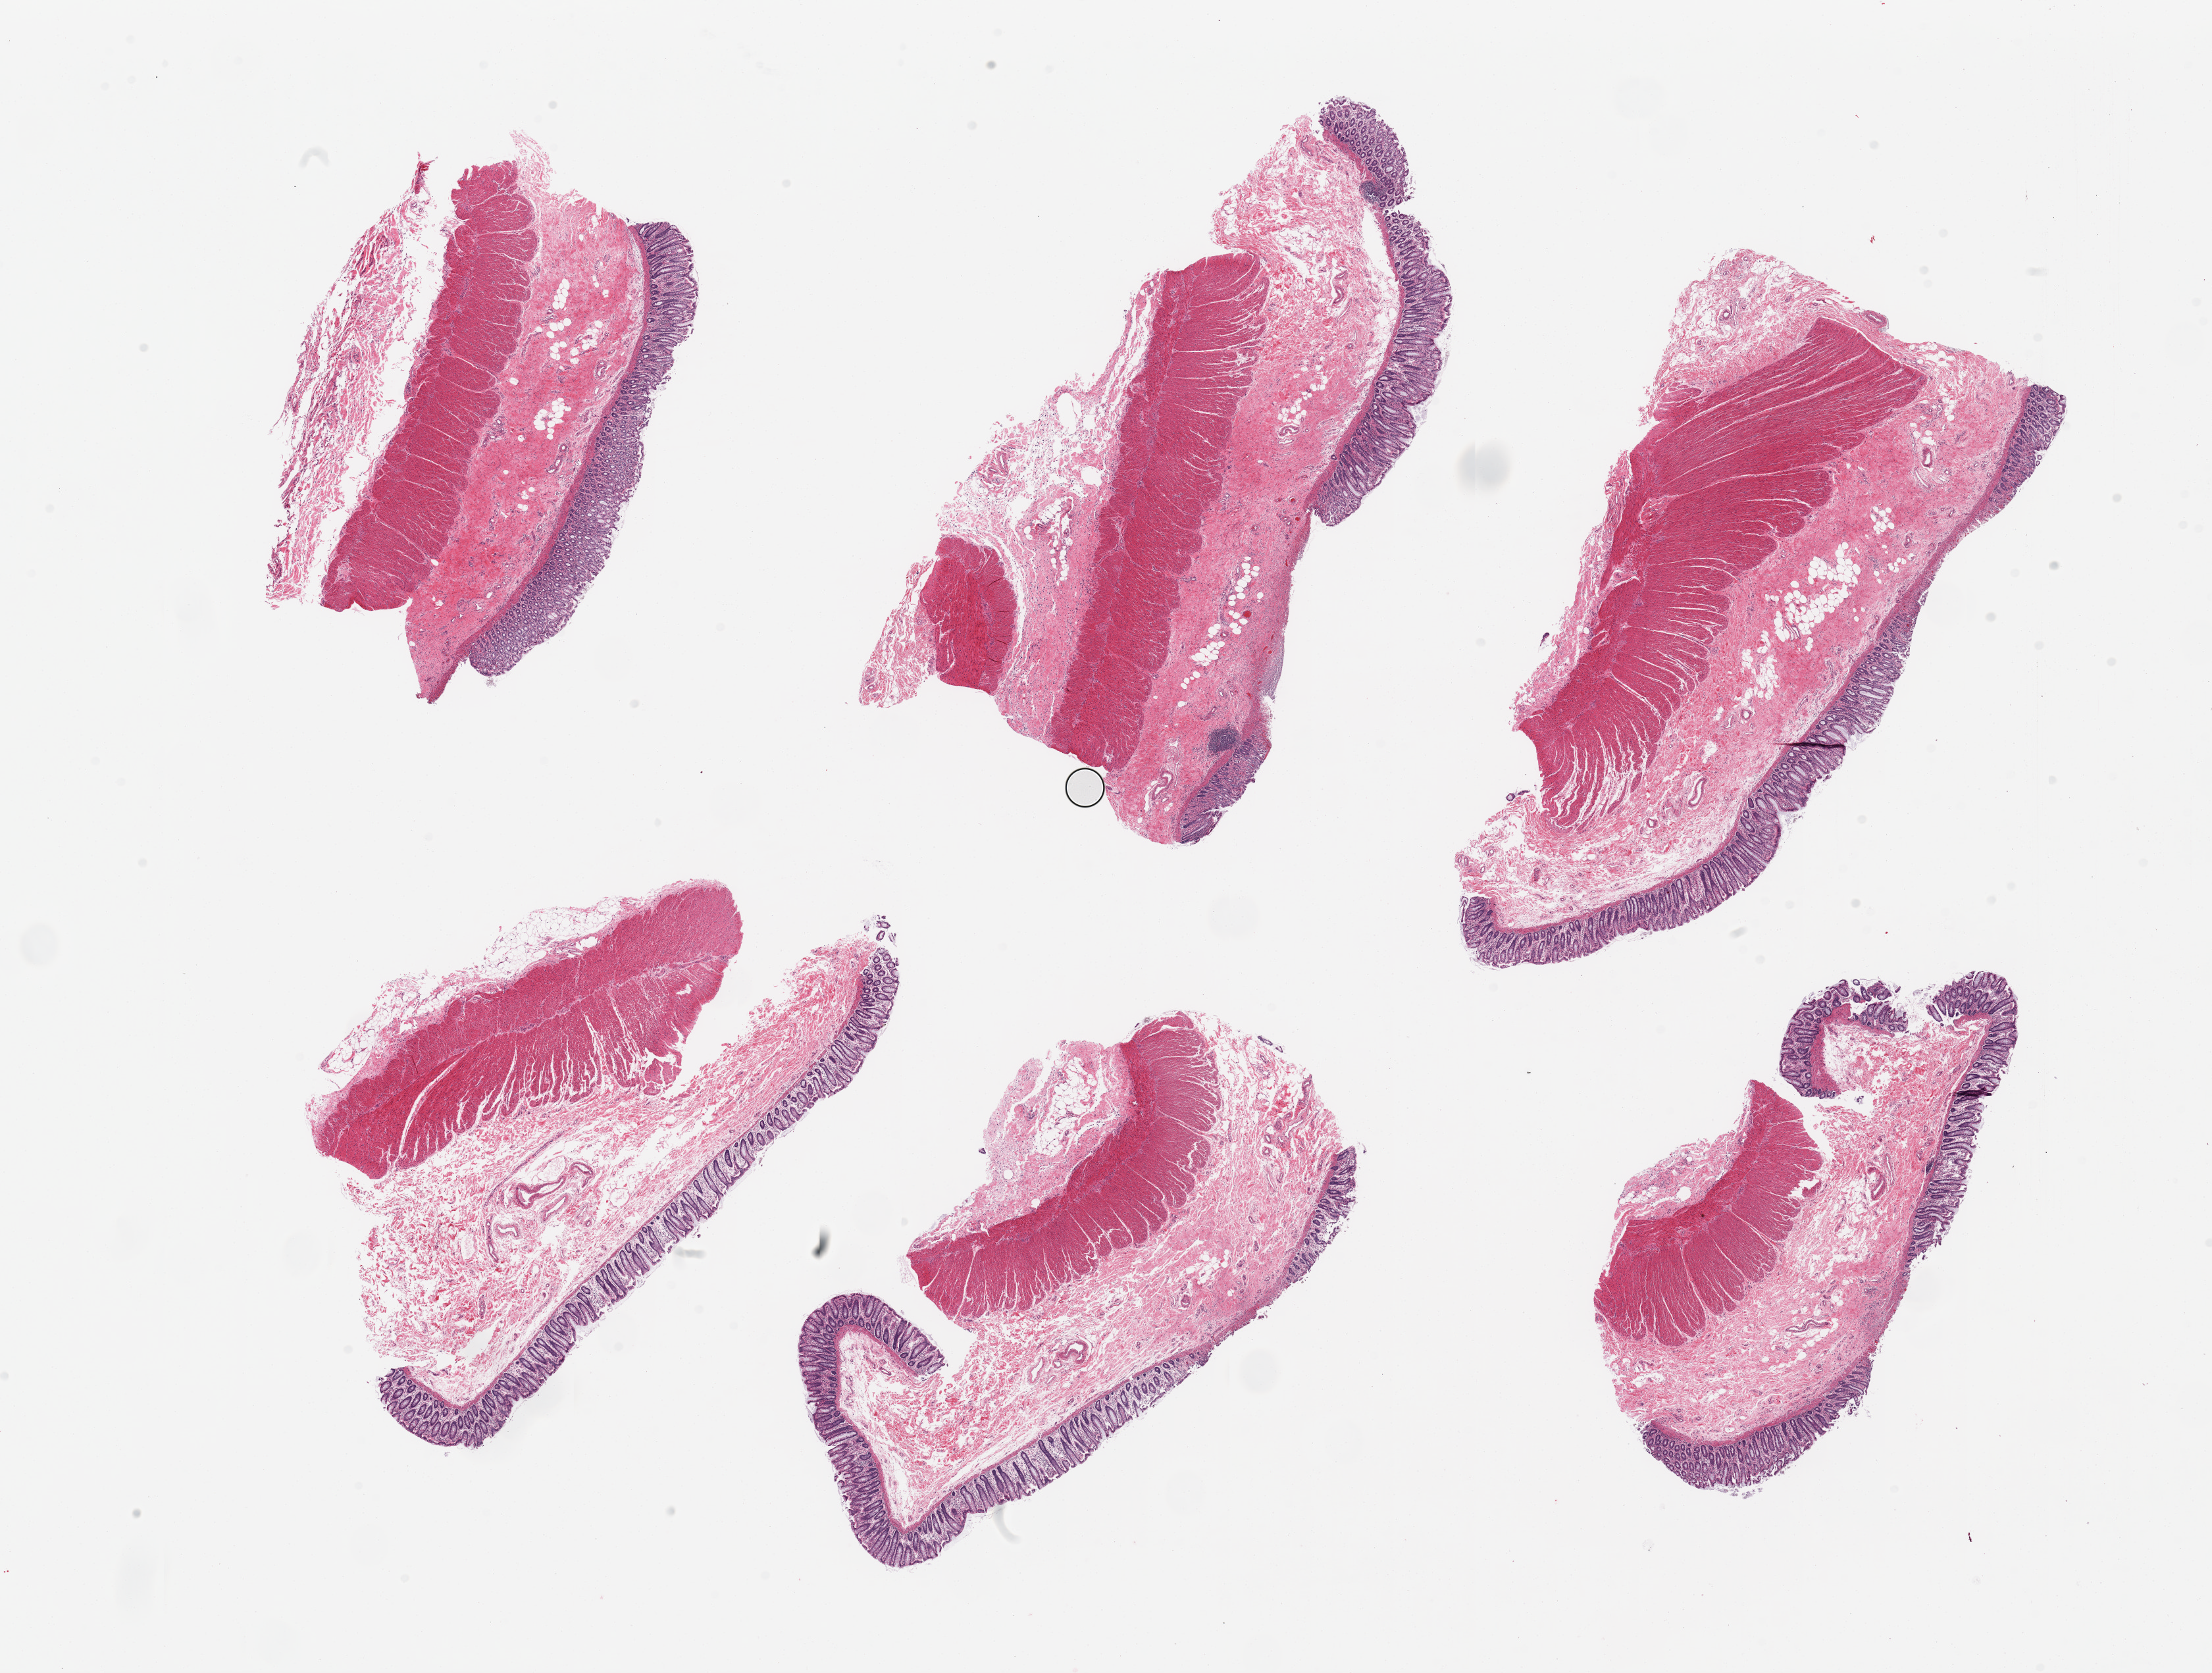
Whole-slide image, H&E stain, brightfield, whole scanned area (about 26.6 x 20.1 mm, from a 20x scan) shown as a low-resolution overview, PAXgene-fixed, paraffin-embedded tissue, section of transverse colon (target tissue), donor tissue sample. Female donor.
- review note (as recorded): 6 pieces; full thickness with some mucosal defects